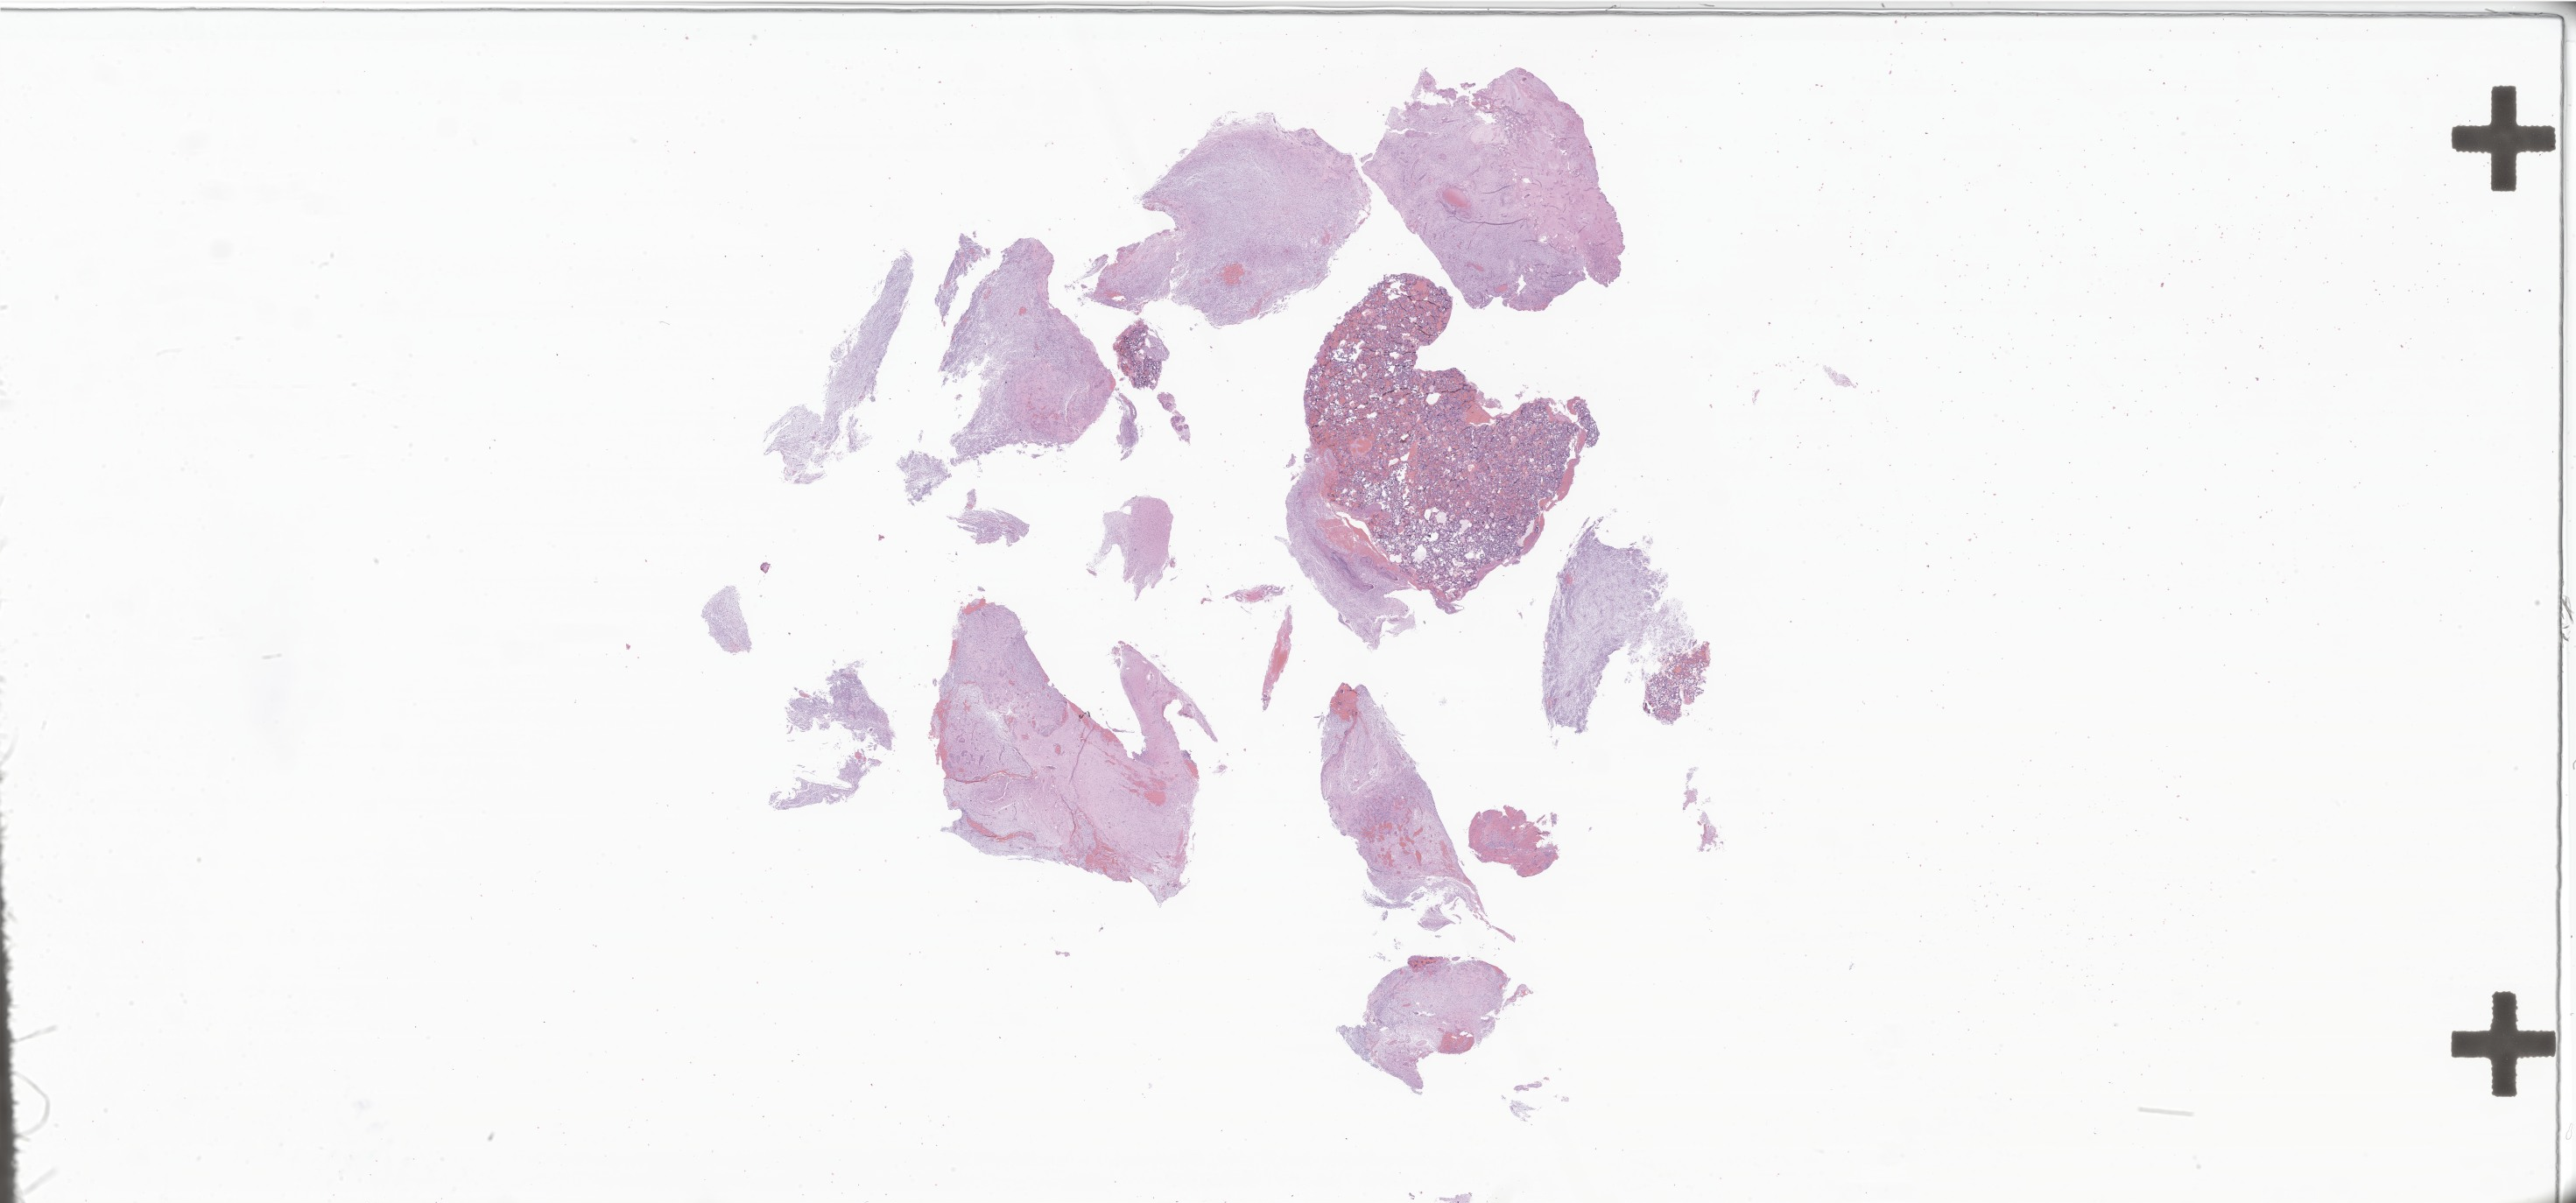
Whole-slide image, H&E stain of tumor tissue from the brain — shown as a low-resolution overview of the whole scanned area (about 49.6 x 23.2 mm). Formalin-fixed paraffin-embedded section. Patient: male, age 186 months.
Recorded diagnosis: Pilocytic astrocytoma.